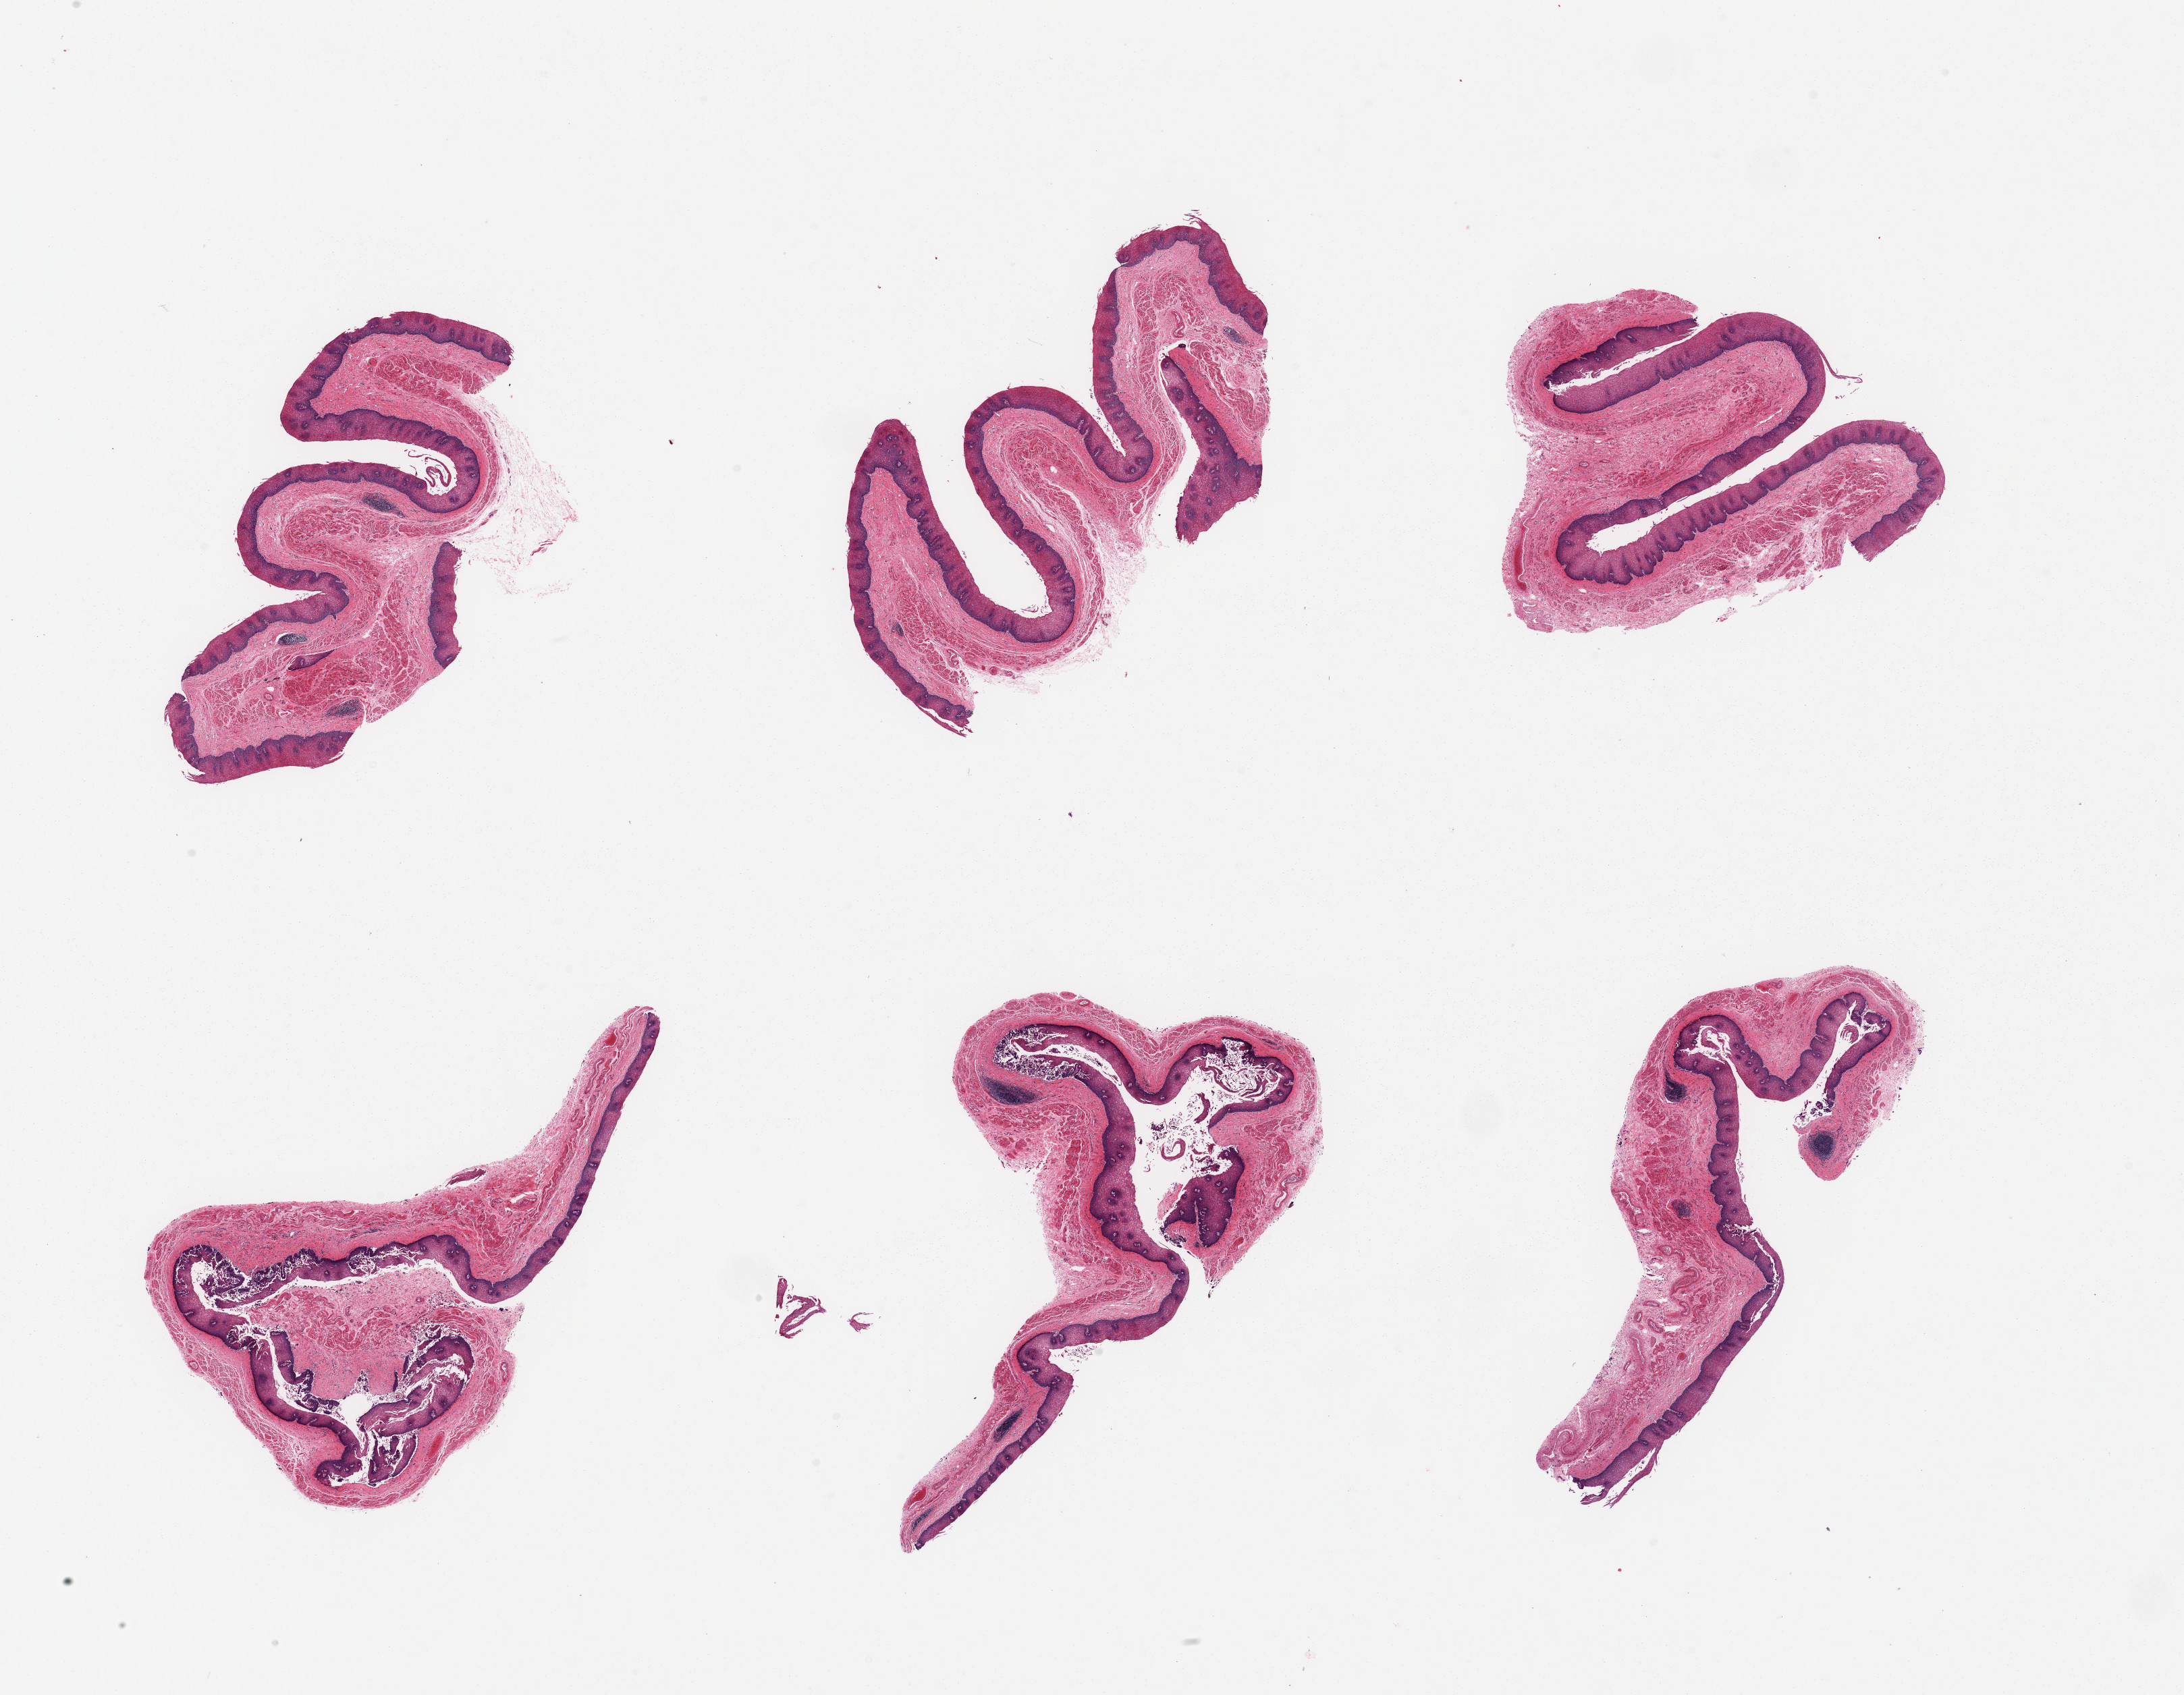
H&E whole-slide image — a low-resolution overview of the entire scanned area, about 25.6 x 19.9 mm (acquisition: 20x scan), PAXgene-fixed, paraffin-embedded tissue, target tissue: esophageal mucous membrane, tissue donor sample. Male donor.
- pathologist's review note for this sample: 6 pieces; 3 well preserved; 3 have squamous fragmentation